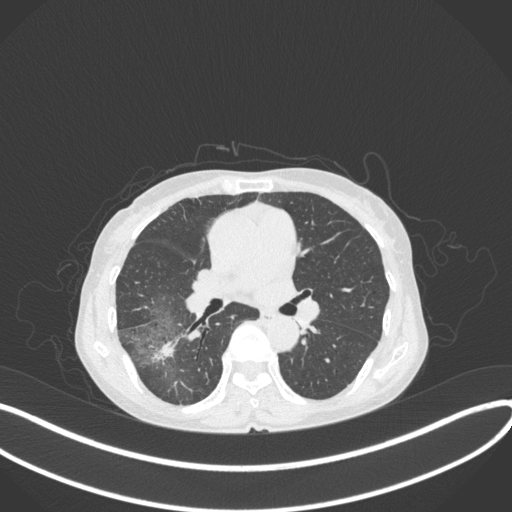
Chest CT, one axial slice. Slice 217 of 379 in the series (ordered by position). Reconstruction kernel B31f. Lung window (W 1500 / L -600 HU). 1 mm slice thickness. 512 × 512 image matrix, field of view 400 × 400 mm. Patient: female, 69 years. From the clinical record (not read from this slice): clinical TNM (as recorded): T1b N0 M0; histopathological grade: G2-3.
Outlined on this slice (bounding box drawn by a radiologist):
- lung tumour (recorded histology: adenocarcinoma): bounding box (x1, y1, x2, y2) in pixels: (149, 339, 180, 365)